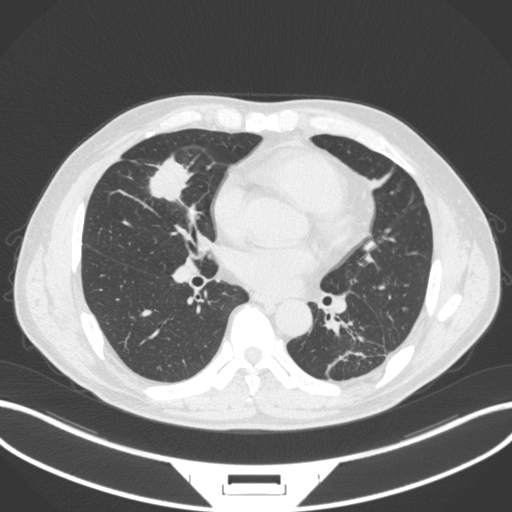
Chest CT, one axial slice; position 138 of 399 along the scan axis; reconstruction kernel B31f; 120 kVp; lung window (W 1500 / L -600 HU); 1 mm slice thickness; 512 × 512 image matrix, field of view 400 × 400 mm. Male patient, age 59 years. Case-level facts recorded for this patient, not image findings: clinical TNM (as recorded): T2a N1 M0.
Structures marked on this image (rectangle marked by the reading radiologist):
- lung tumour (recorded histology: adenocarcinoma): bounding box (x1, y1, x2, y2) in pixels: (144, 156, 194, 207)